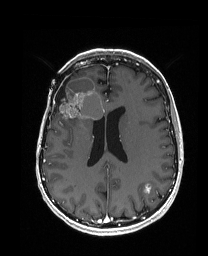
Brain MRI from a brain-tumour surgery series, one axial slice; position 76 of 192 along the scan axis; T1-weighted post-contrast; 1 mm slice thickness; 208 × 256 image matrix, field of view 203 × 250 mm. From the clinical record (not read from this slice): histopathology: Metastatic Carcinoma from Breast primary; tumour location: Right Frontal.
Structures marked on this image (outlined manually by an expert reader):
- previous resection cavity: box from (x=54, y=77) to (x=71, y=112) px
- tumour: (x=55, y=77)–(x=104, y=128)